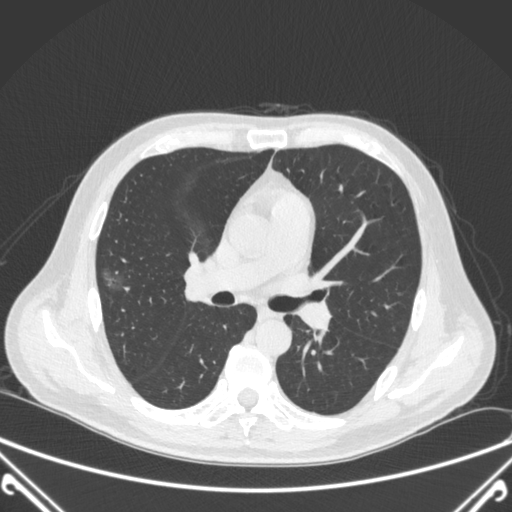
Chest CT, one axial slice. Slice 218 of 360 in the series (ordered by position). Lung window (W 1500 / L -600 HU). 1 mm slice thickness. 512 × 512 image matrix, field of view 380 × 380 mm. Patient: male, 64 years. Case-level facts recorded for this patient, not image findings: clinical TNM (as recorded): T1c N0 M0; histopathological grade: G2.
Outlined on this slice (bounding box drawn by a radiologist):
- lung tumour (recorded histology: adenocarcinoma): bounding box (x1, y1, x2, y2) in pixels: (105, 265, 134, 298)